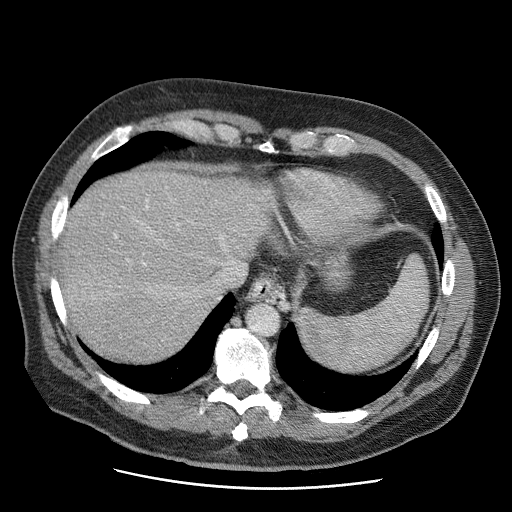
Contrast-enhanced abdominal CT (liver protocol), one axial slice. Slice 50 of 81 in the series (ordered by position). Reconstruction kernel STANDARD. 120 kVp. Soft-tissue window (W 400 / L 40 HU). 2.5 mm slice thickness. 512 × 512 image matrix, field of view 380 × 380 mm. From the clinical record (not read from this slice): diagnosis: hepatocellular carcinoma (patient treated with transarterial chemoembolisation; whether this scan precedes or follows treatment is not stated here); TNM stage (as recorded): Stage-IIIA; Child-Pugh class: A; tumour differentiation: moderately differentiated; tumour size: 5.5 cm.
Outlined on this slice (semi-automatically segmented with operator editing):
- liver parenchyma outside the tumour (the mass and vessels are separate outlines, so this box may not span the whole liver): box from (x=58, y=168) to (x=276, y=362) px
- liver vessels: (x=115, y=206)–(x=178, y=238)